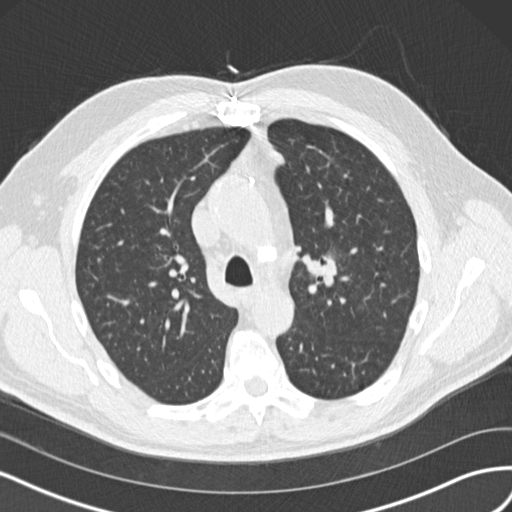
Chest CT (low-dose screening protocol), one axial image. First (baseline) screen. Lung window (W 1500 / L -600 HU). 2 mm slice thickness. Standard (soft-tissue) reconstruction kernel (B30f). 120 kVp. Slice 51 of 160 in the series. 512 × 512 image matrix, field of view 360 × 360 mm. Male participant, aged 65 years at enrolment. Former smoker at enrolment.
Expert-annotated lung lesion, bounding box [x1, y1, x2, y2] px = [300, 243, 354, 297]. The screening reader recorded 4 non-calcified nodules or masses ≥4 mm on this exam (left upper lobe, left upper lobe, right upper lobe, right middle lobe); which of them this box marks is not recorded. Official screen result: positive, change unspecified: nodule(s) >= 4 mm or enlarging nodule(s), mass(es), or other non-specific abnormalities suspicious for lung cancer. Participant outcome: lung cancer diagnosed 945 days after this screen — acinar cell carcinoma, left upper lobe, stage IA (AJCC 6th edition), 25 mm at pathology.